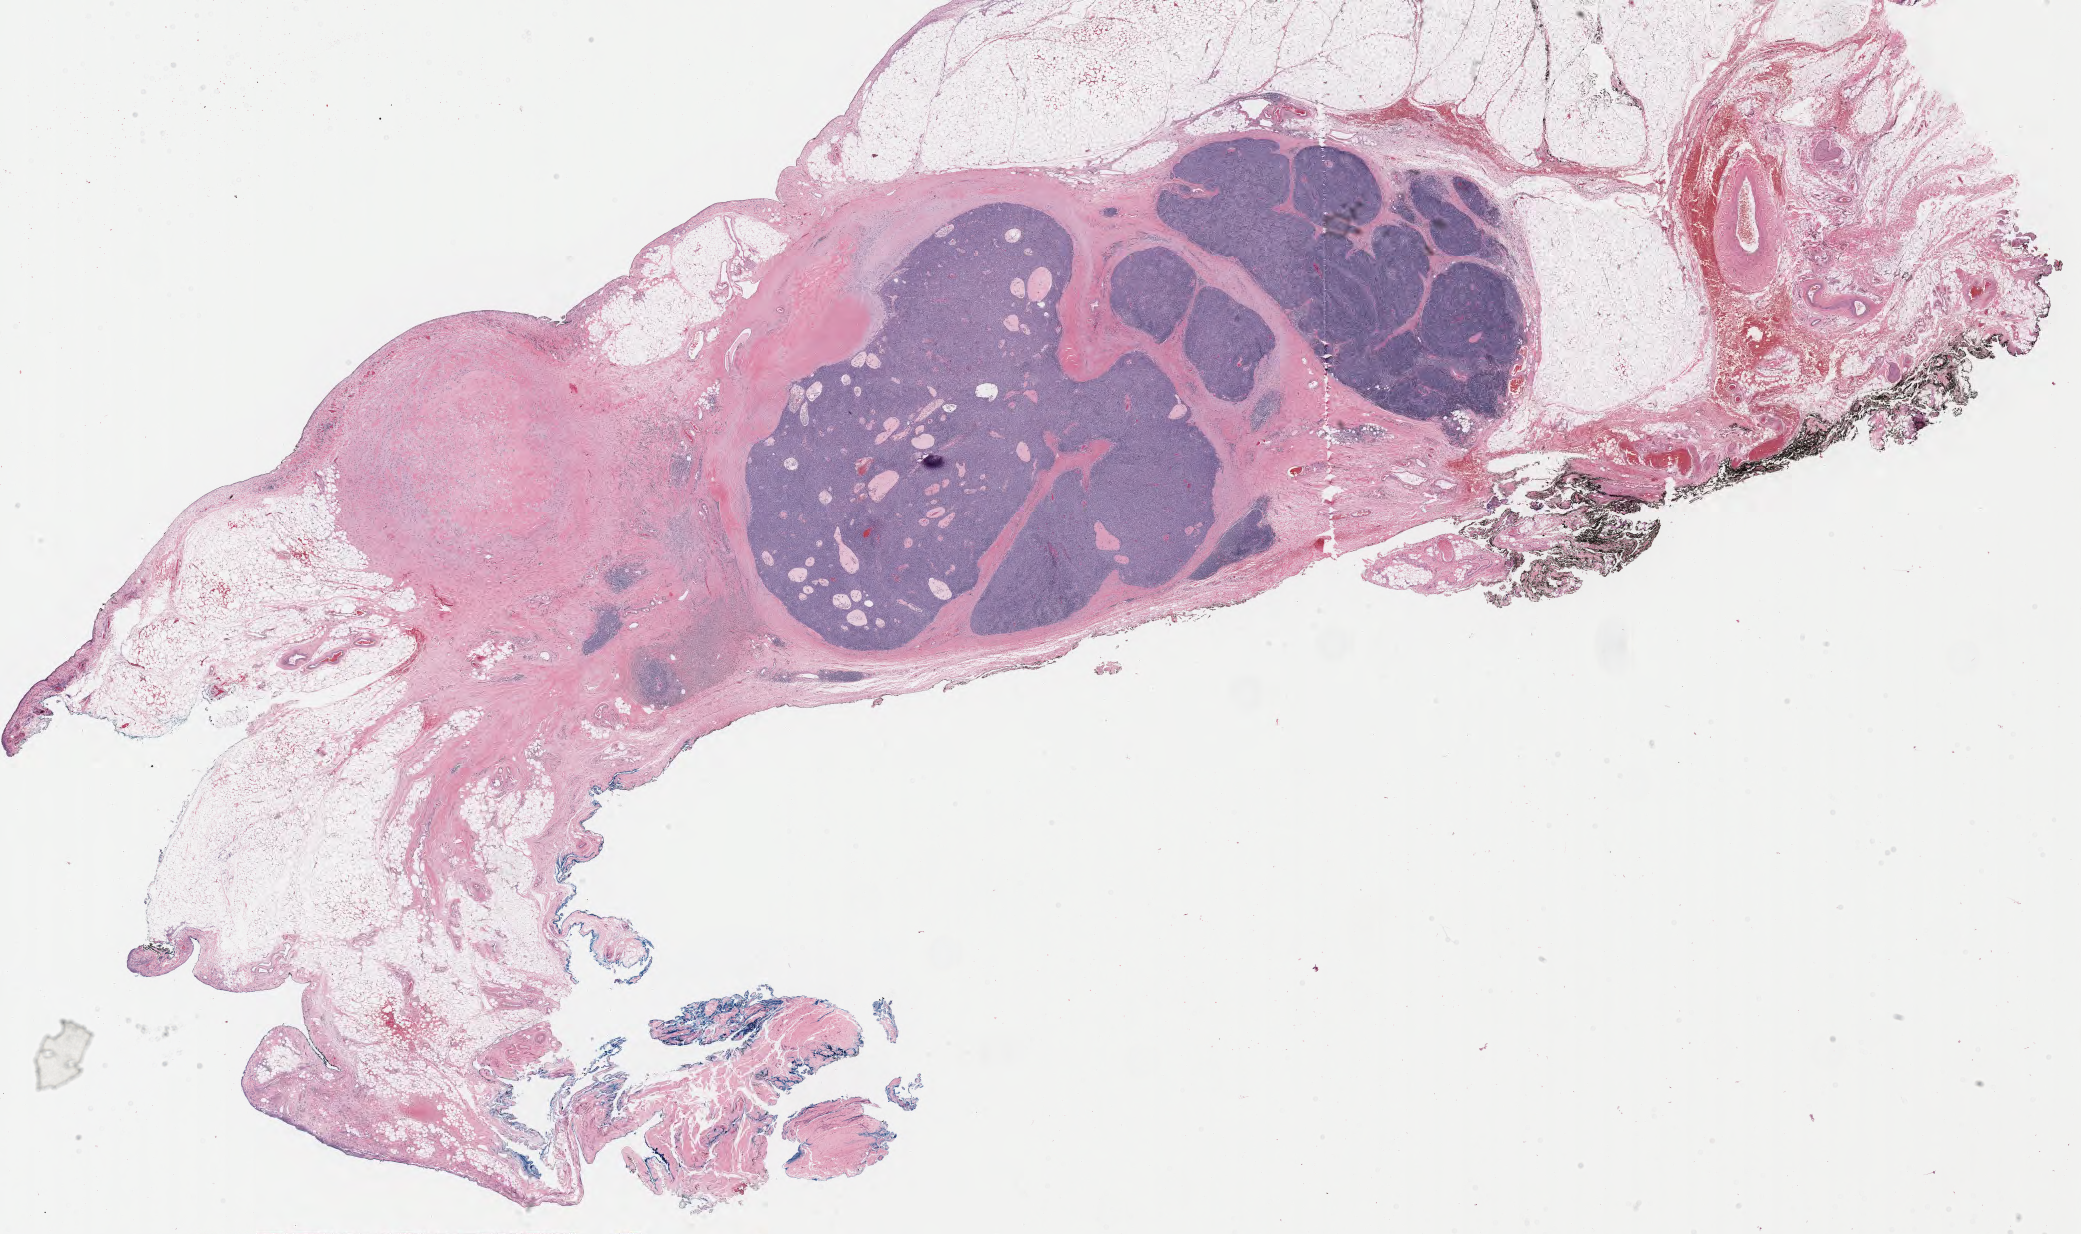
Whole-slide histology image, Hematoxylin and eosin (H&E) stained, shown as a low-resolution overview of the whole scanned area (about 33.0 x 19.6 mm, from a 40x scan). FFPE section. Primary tumour sample from the thymus. Female patient; age at initial diagnosis 43 years.
Histologic diagnosis: Thymoma, type B2, malignant.